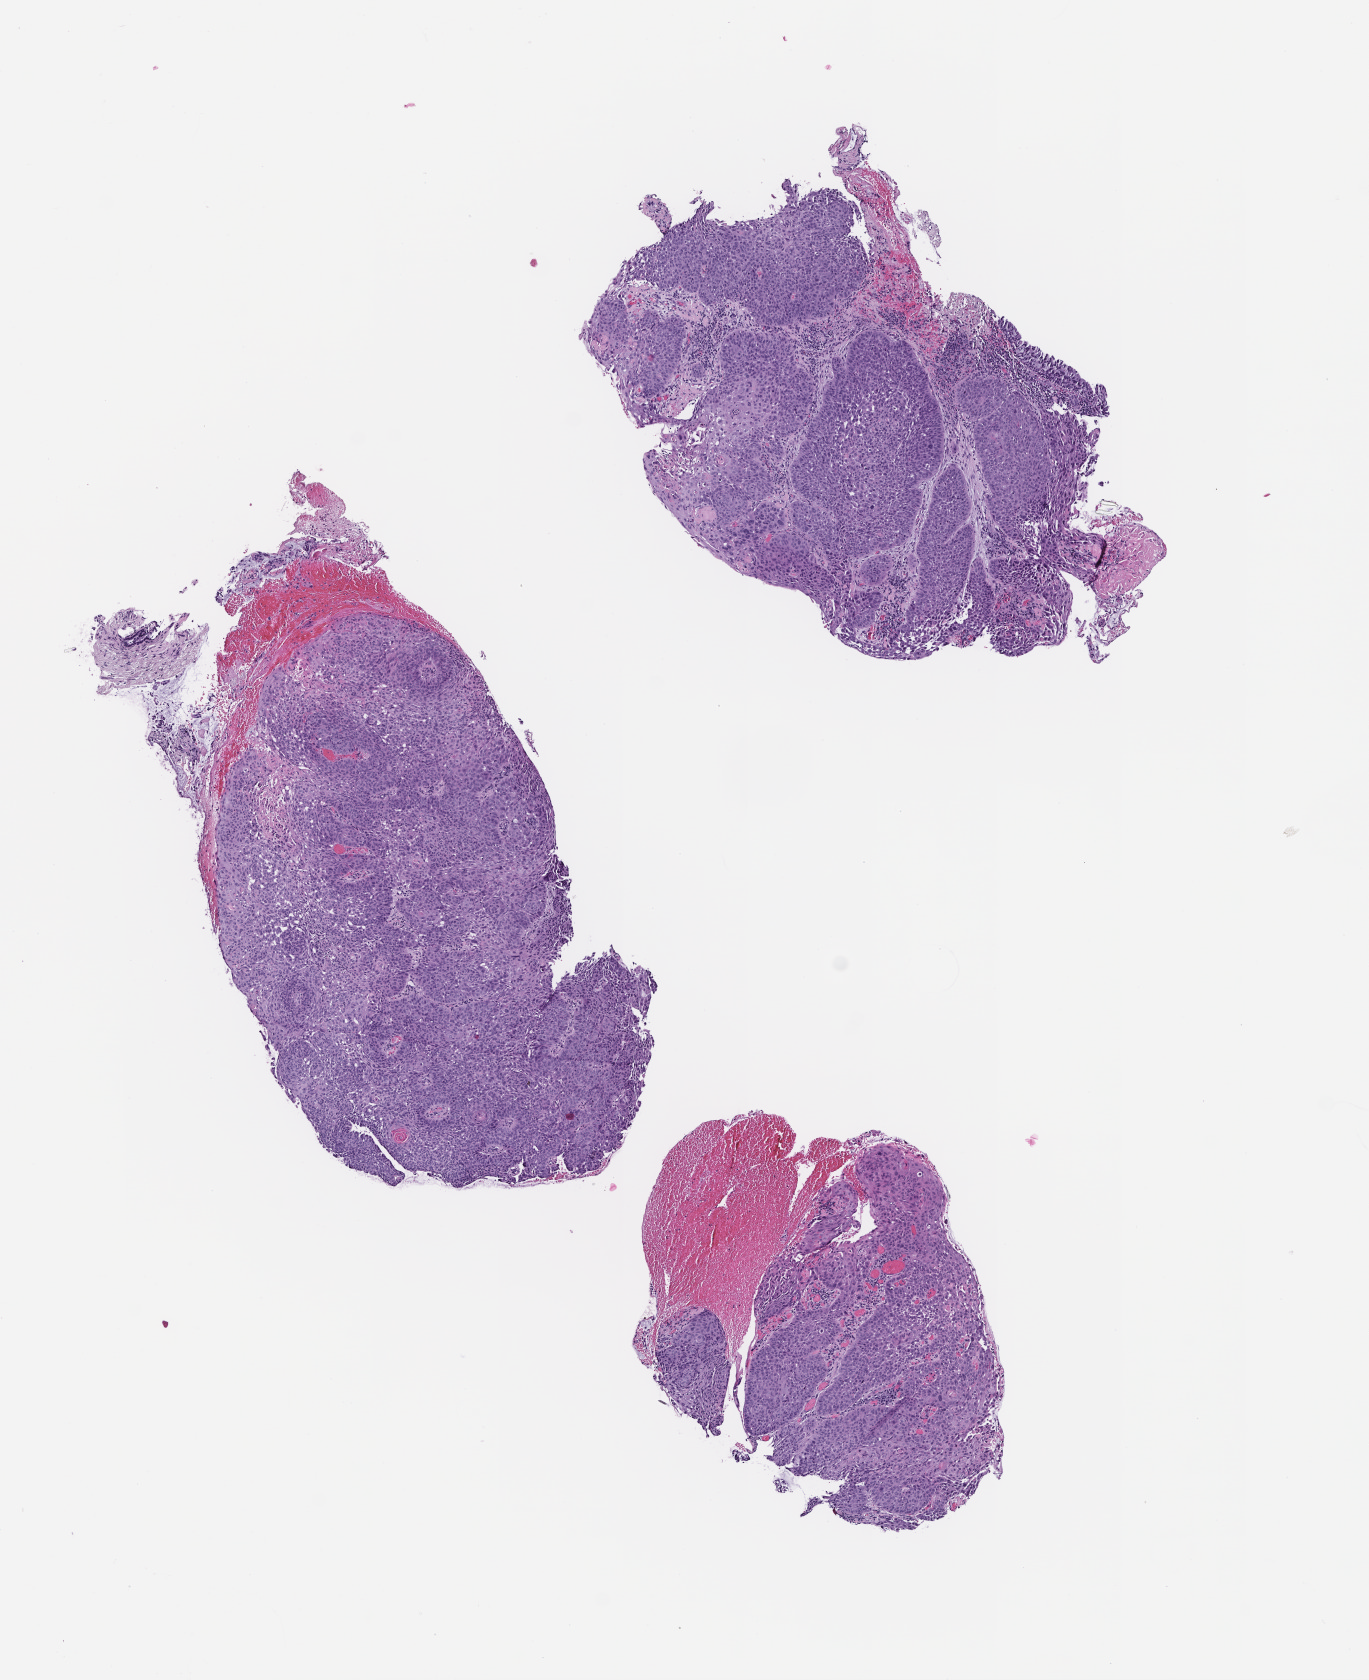
H&E whole-slide image, shown as a low-resolution overview of the whole scanned area (about 5.5 x 6.8 mm), formalin-fixed paraffin-embedded section, site: lung, specimen time point: archival tissue. Patient sex: male.
This section: primary tumor. Diagnosis: Non-Small Cell Lung Carcinoma.